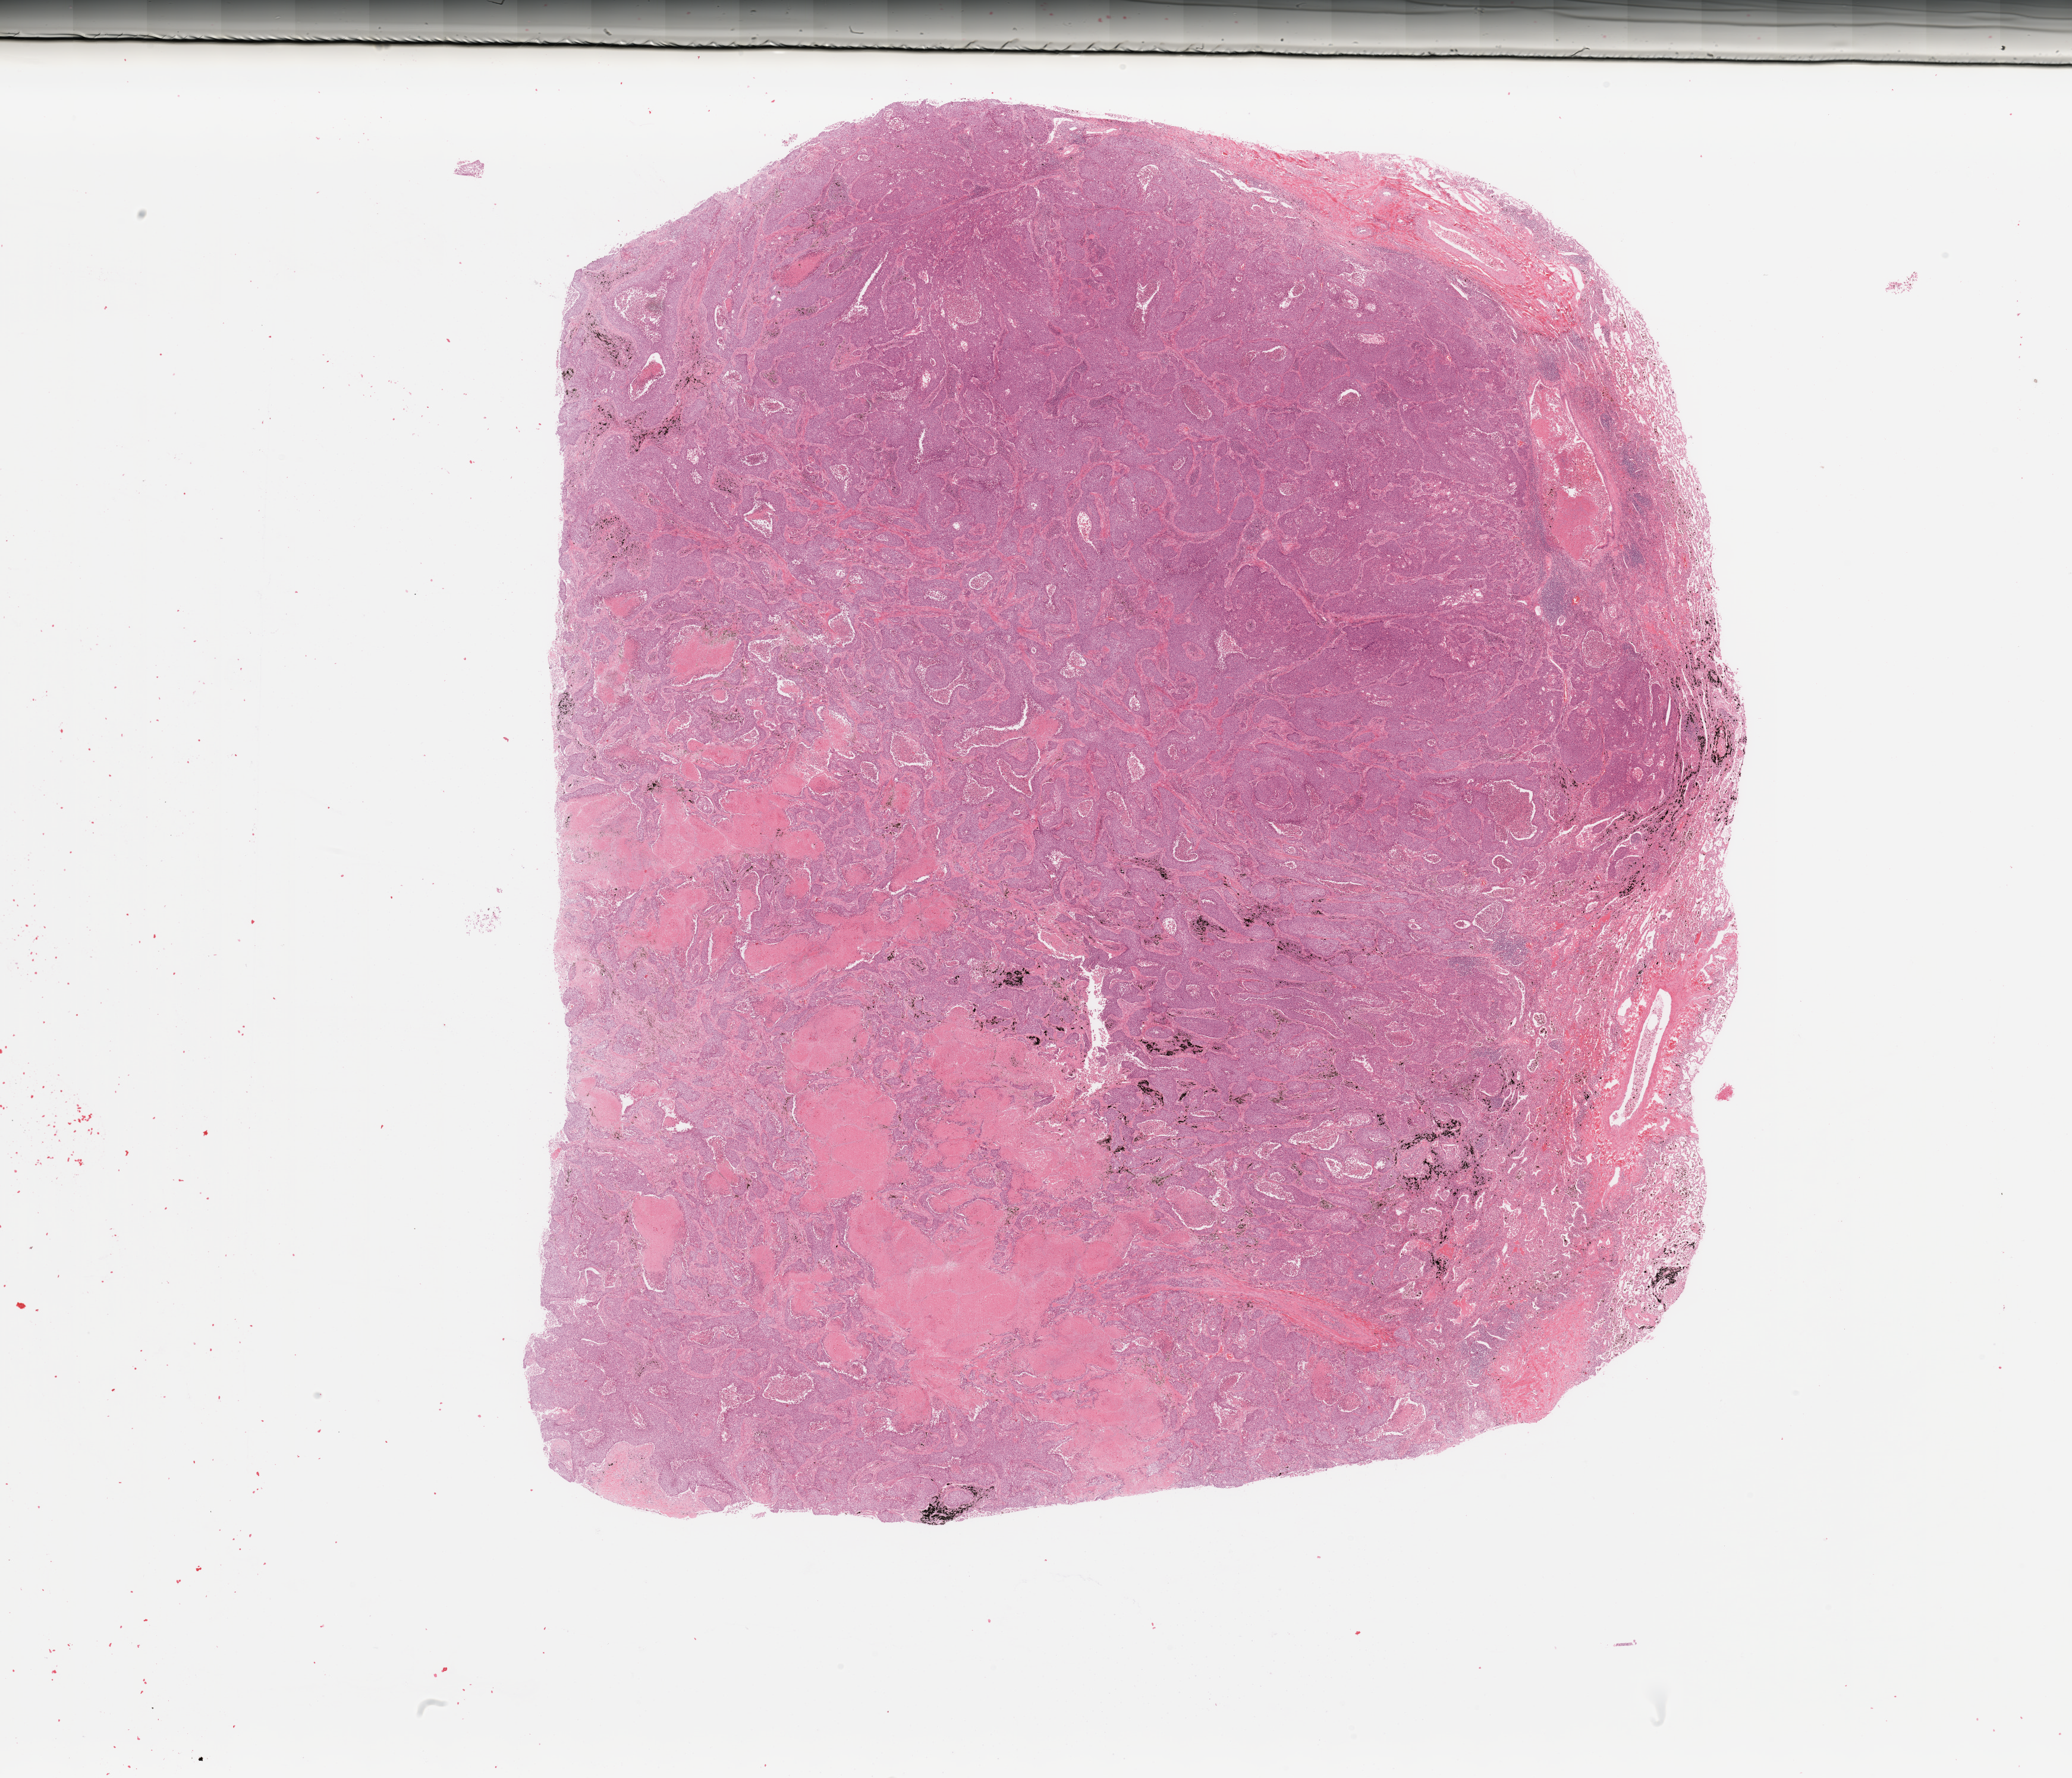
Hematoxylin and eosin (H&E) stained whole-slide image — shown as a low-resolution overview of the whole scanned area (about 27.6 x 23.7 mm, acquisition: 20x scan), lung, tumour tissue. 52-year-old male patient. Histologic grade: G3 (poorly differentiated).
AJCC pathologic stage: IIB. Histologic diagnosis: Squamous cell carcinoma, NOS.